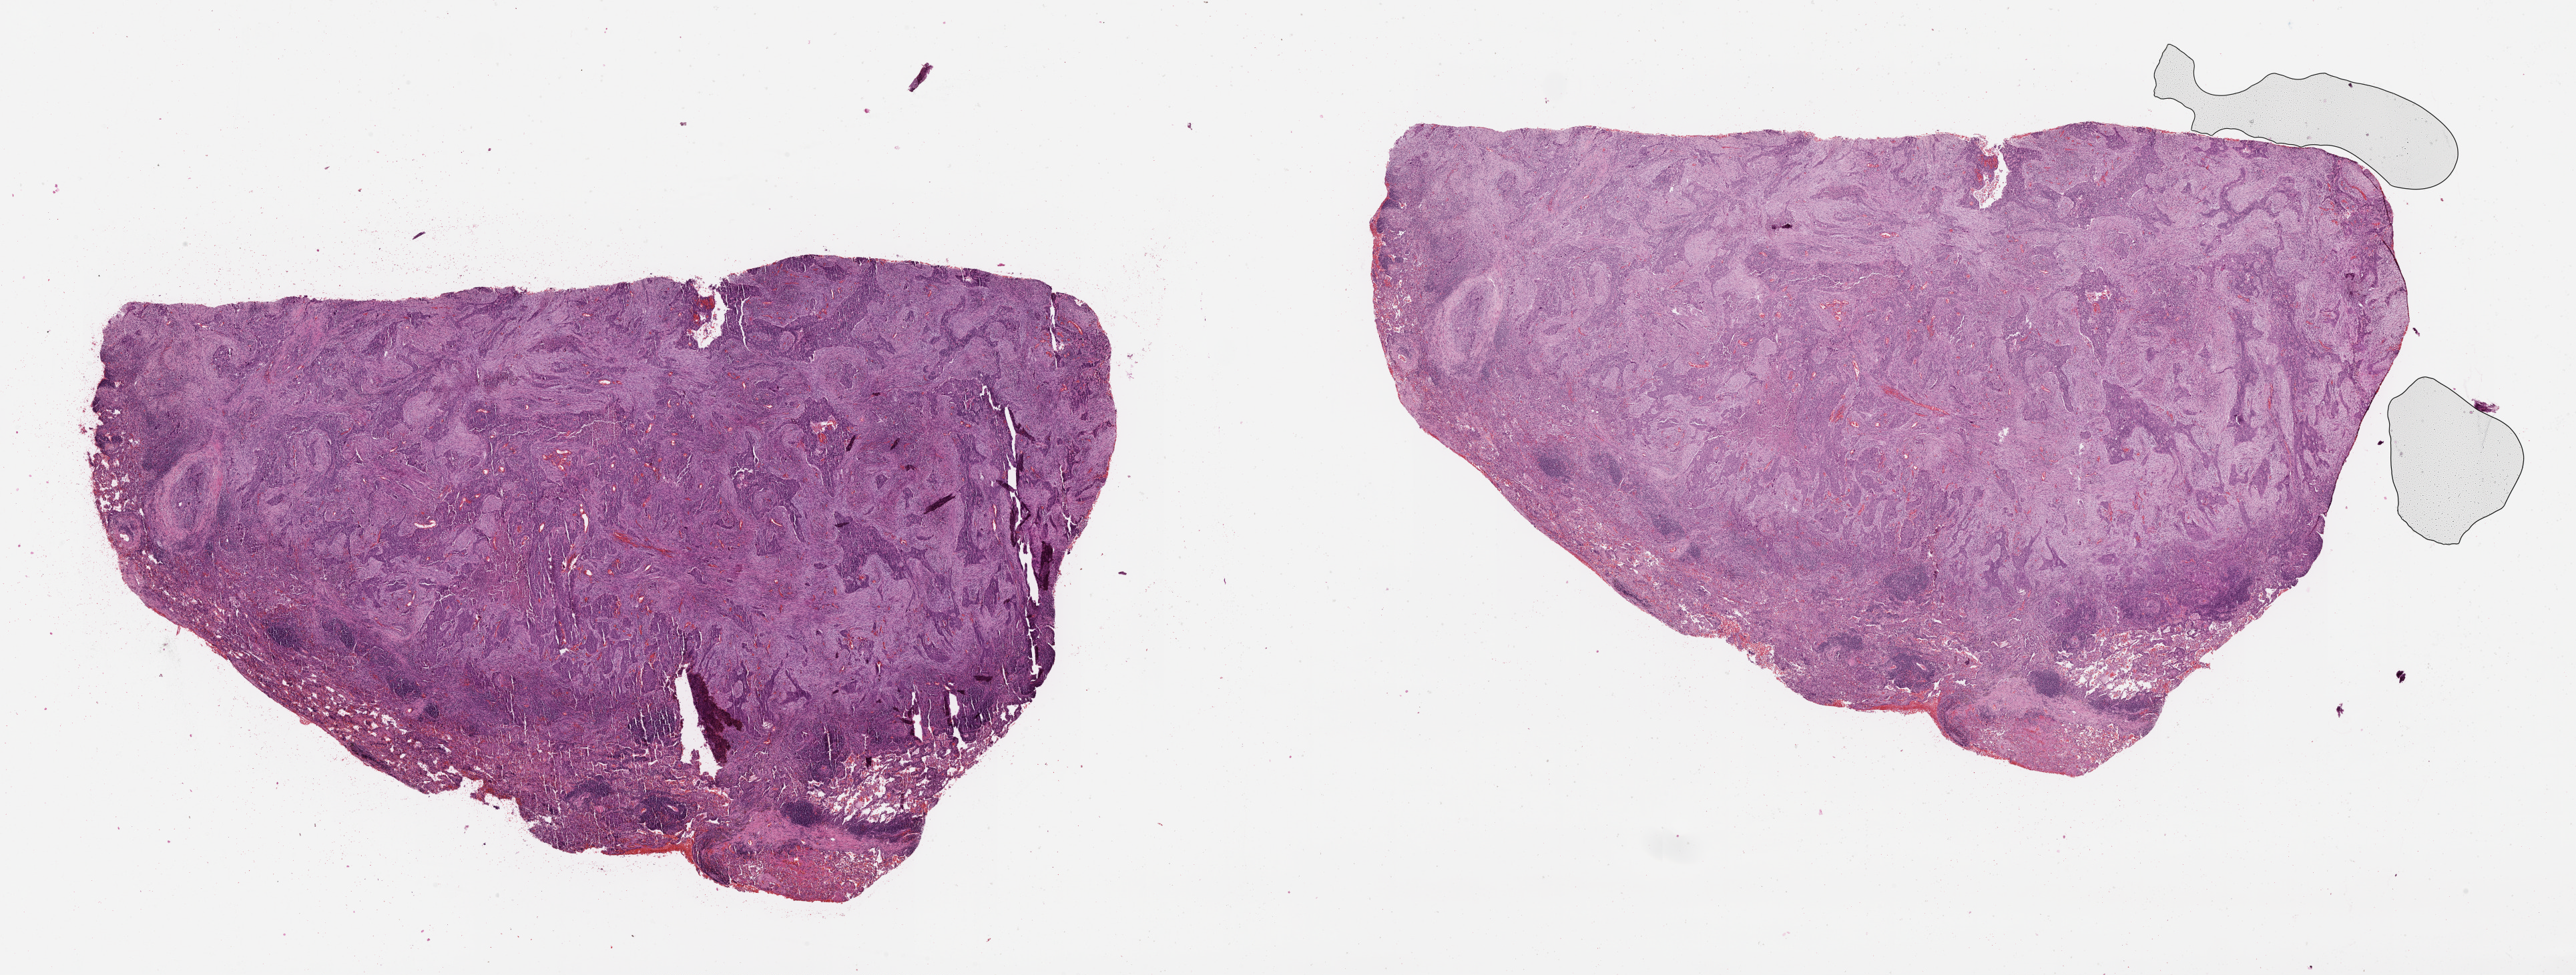
H&E-stained whole-slide image — whole scanned area (about 31.1 x 11.8 mm, slide scanned at 20x) shown as a low-resolution overview, tumour tissue sample, lung. Patient: female, age 62 years.
• patient diagnosis (cohort enrolment): squamous cell carcinoma (lung)